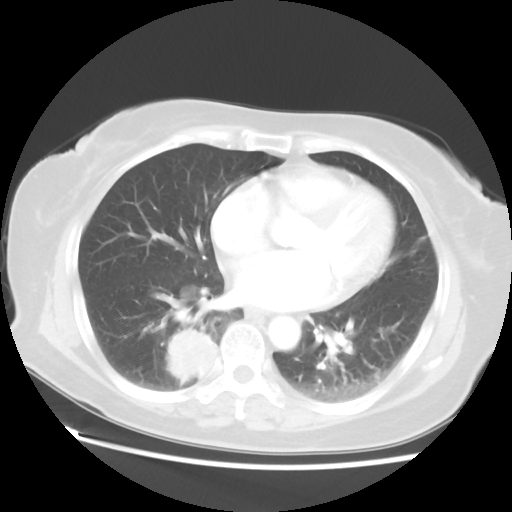
Chest CT, one axial slice. Slice 23 of 52 in the series (ordered by position). Reconstruction kernel STANDARD. 120 kVp. Lung window (W 1500 / L -600 HU). 5 mm slice thickness. 512 × 512 image matrix, field of view 356 × 356 mm. Female patient, age 69 years. Case-level facts recorded for this patient, not image findings: clinical TNM (as recorded): T2 N1 M1a.
Annotated regions visible in this slice (bounding box drawn by a radiologist):
- lung tumour (recorded histology: adenocarcinoma): bounding box <164,323,221,385> (left, top, right, bottom; pixels)